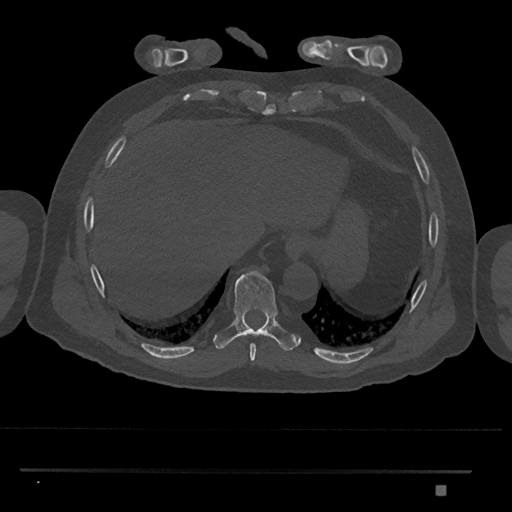
CT including the spine, one axial slice. Slice 1065 of 1134 in the series (ordered by position). Reconstruction kernel Br40s/3. Bone window (W 1800 / L 400 HU). 0.5 mm slice thickness. 512 × 512 image matrix, field of view 429 × 429 mm. Male patient, age 65 years. From the clinical record (not read from this slice): primary cancer: prostate.
Structures marked on this image (semi-automatic segmentation, software-assisted and operator-edited):
- T8 vertebra: bounding box <250,344,256,362> (left, top, right, bottom; pixels)
- T9 vertebra: <214,270,301,351>